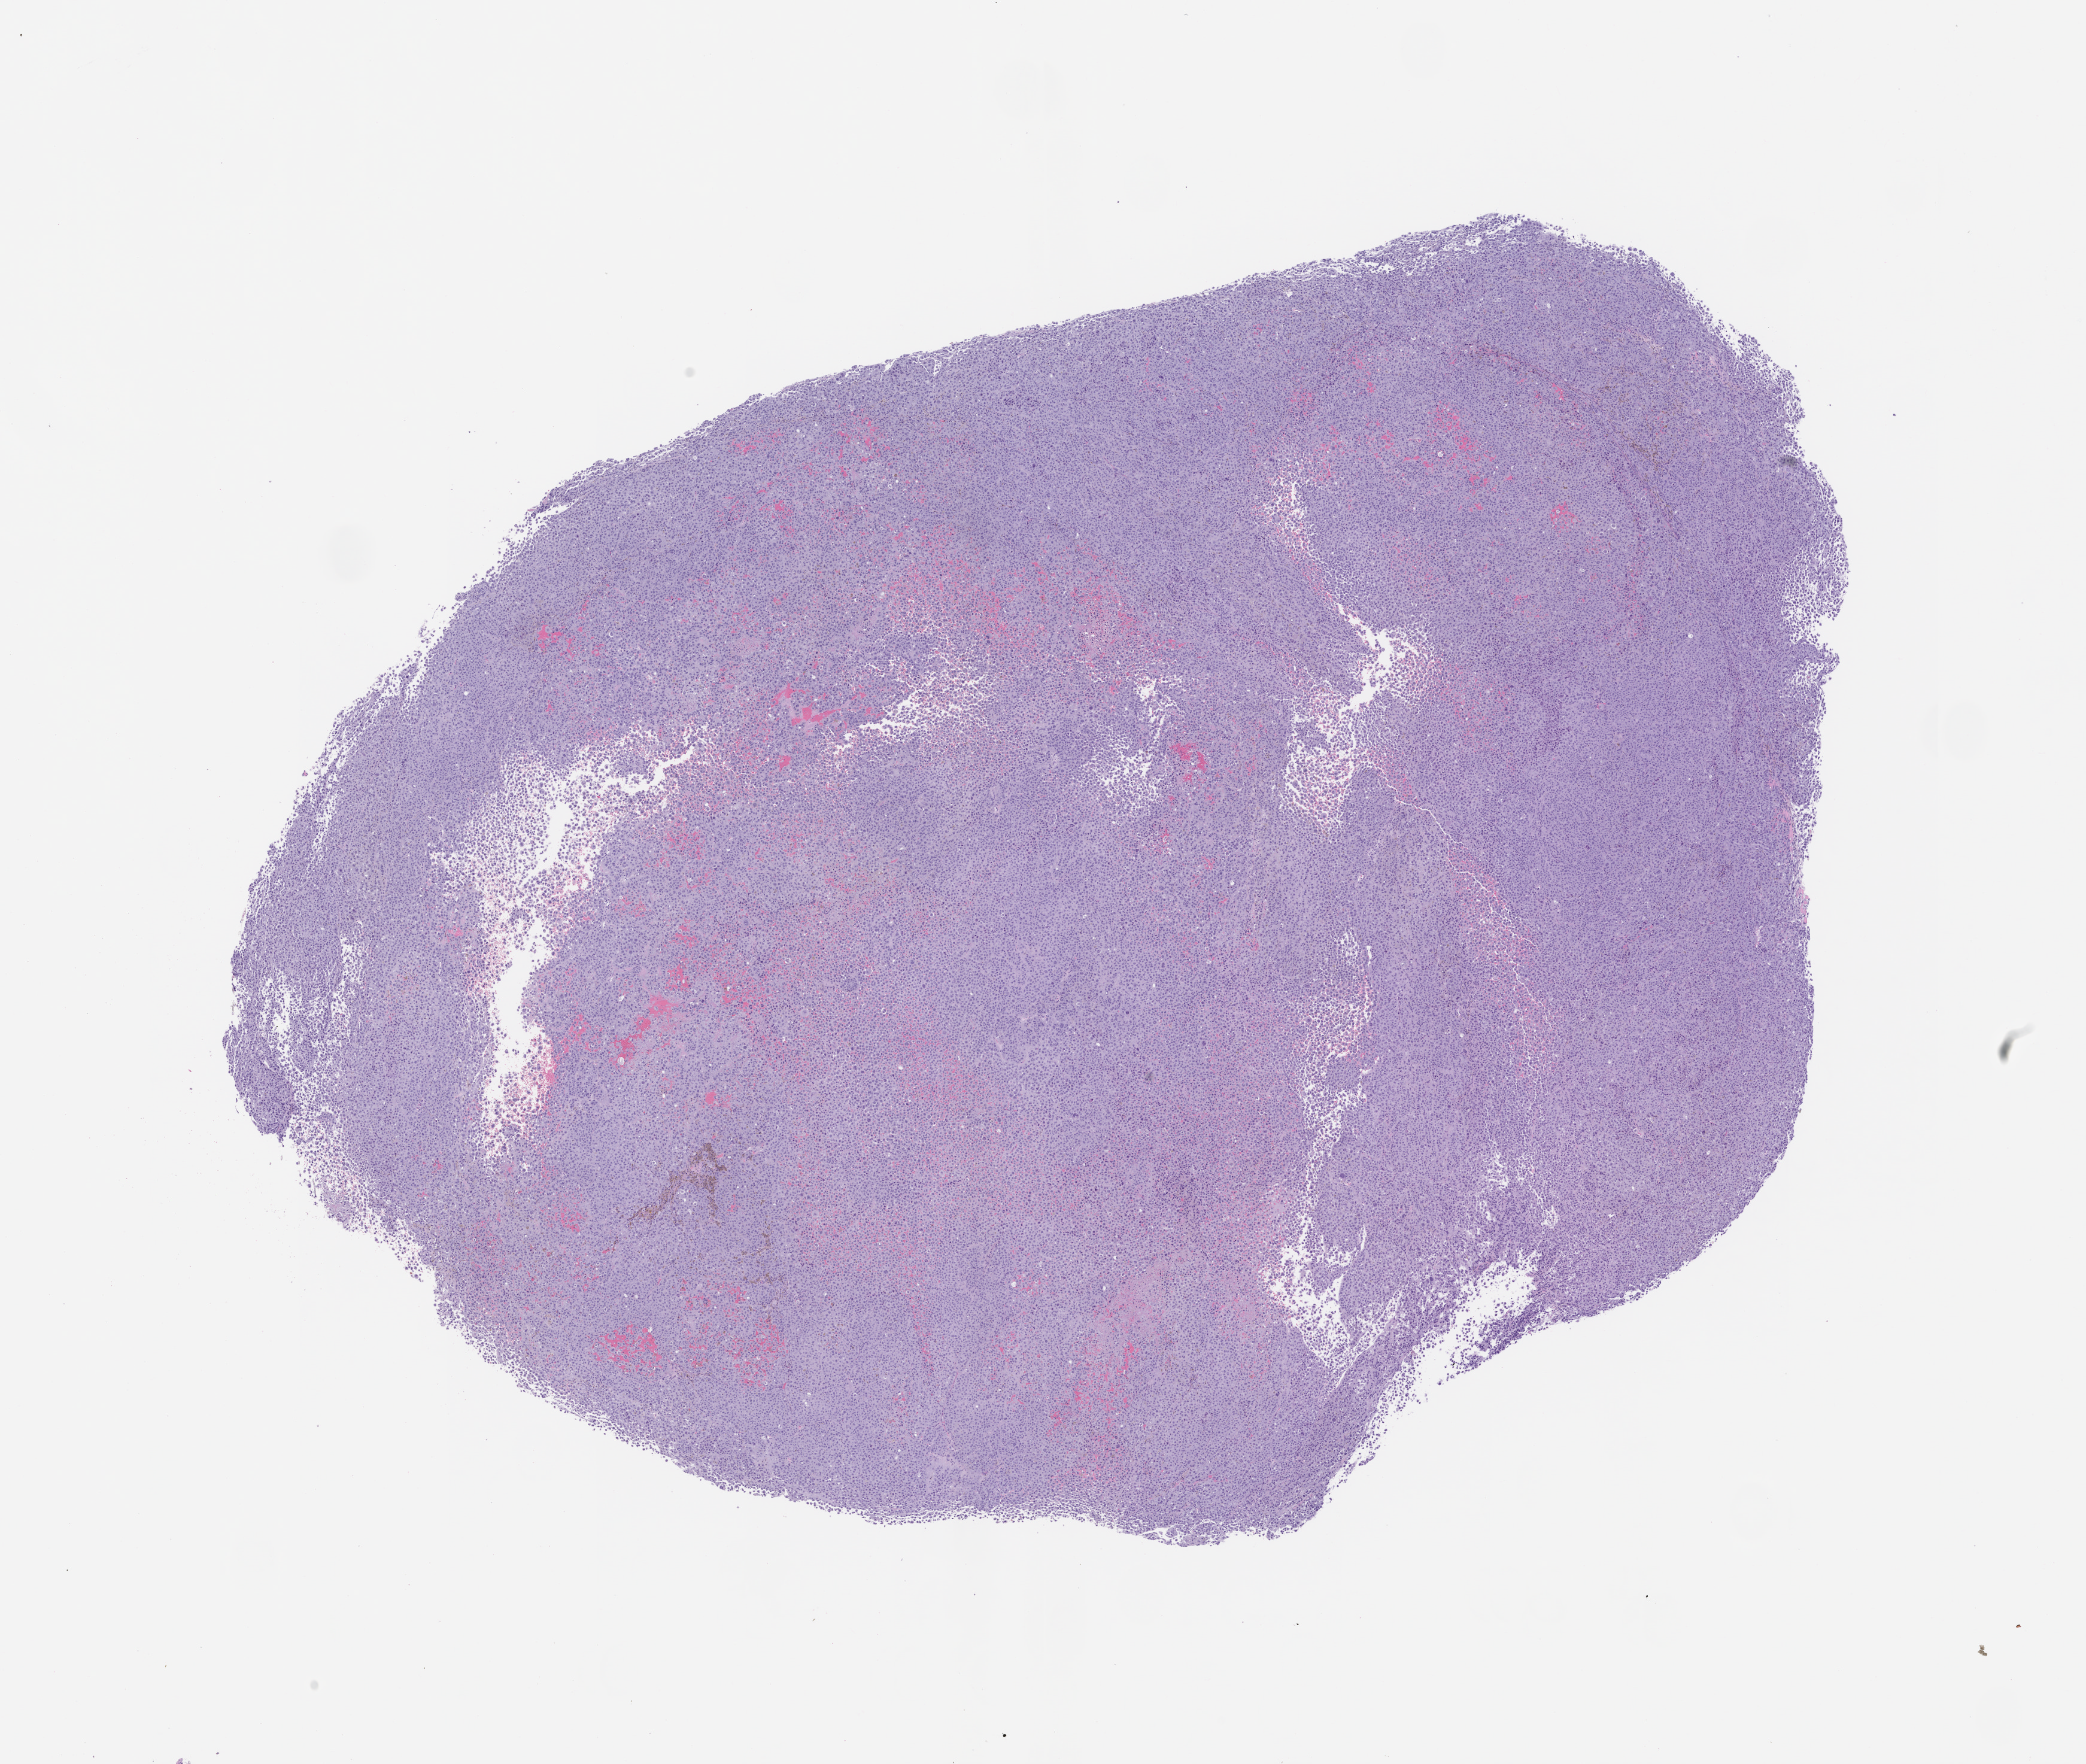
H&E whole-slide image of a patient-derived xenograft (PDX) tumor grown in a mouse, passage 1, whole scanned area (about 14.0 x 11.8 mm) shown as a low-resolution overview, formalin-fixed, paraffin-embedded (FFPE) tissue, tumor site category: skin.
Originating patient diagnosis: Melanoma.